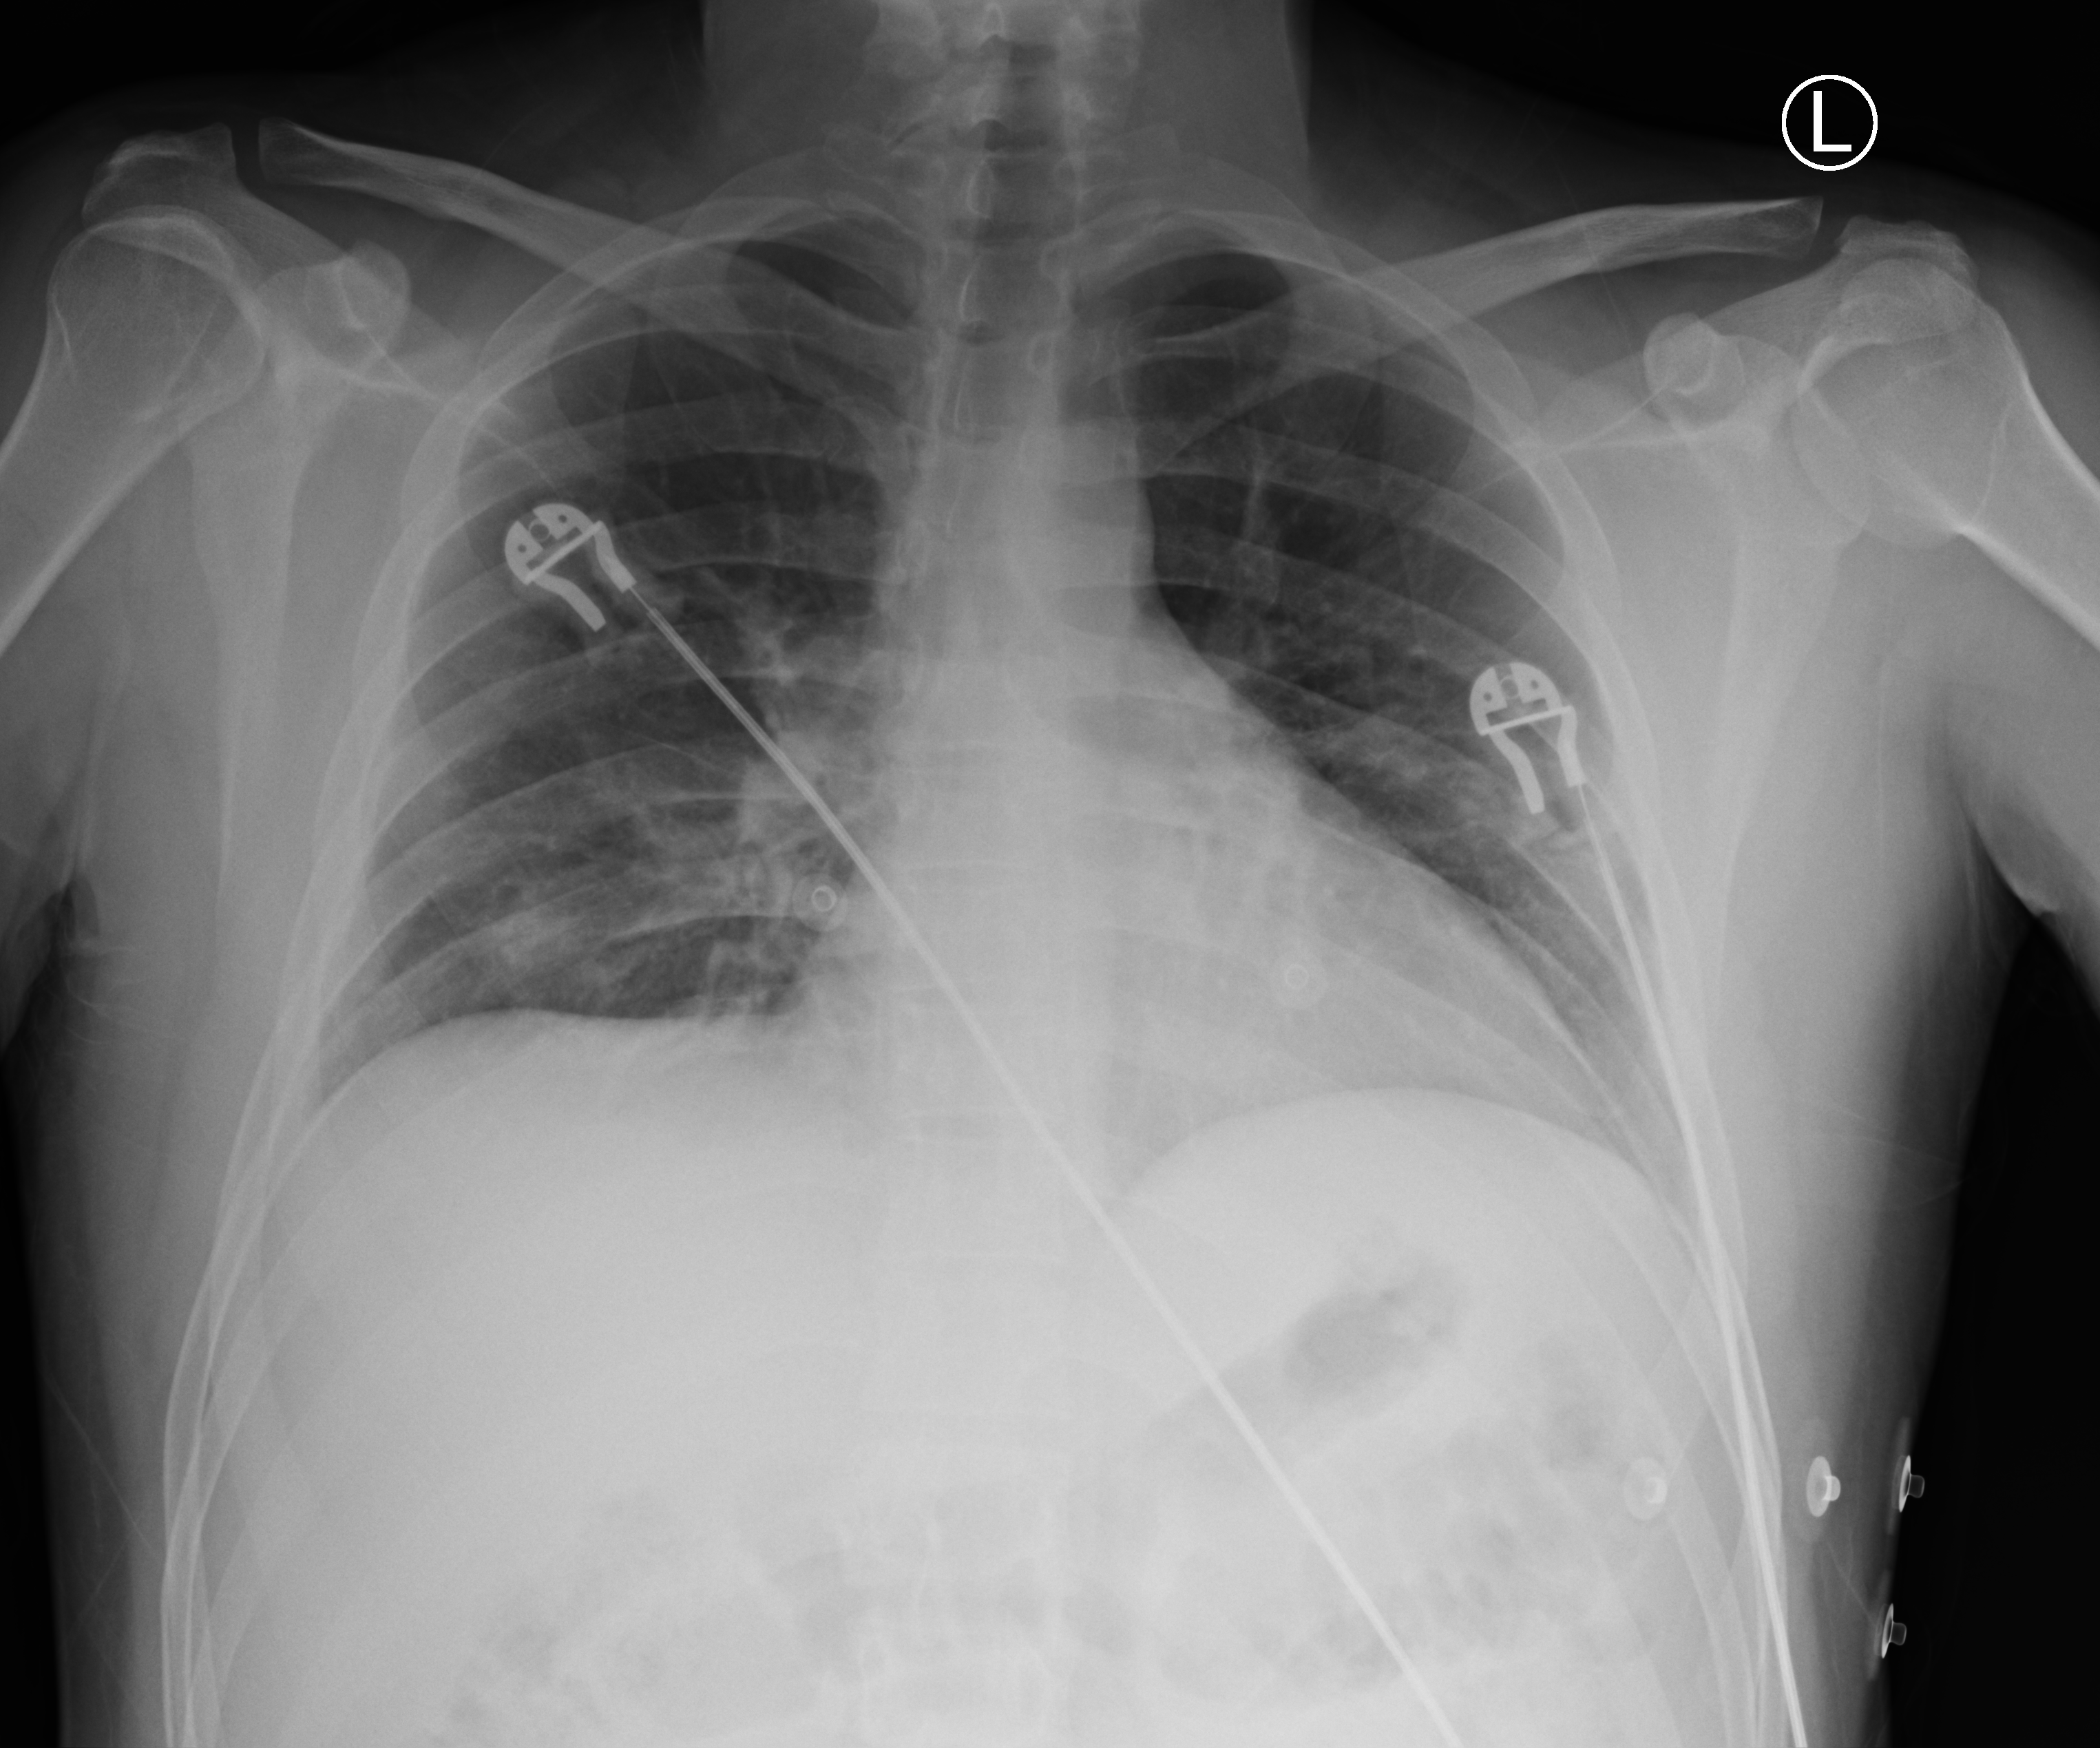
Portable chest radiograph; anteroposterior (AP) projection. Male patient hospitalised with COVID-19, age 18–59 years.
Hospital-stay facts (about this admission, not read from this image; timing relative to this image not recorded): admitted to intensive care during this hospital stay: no.